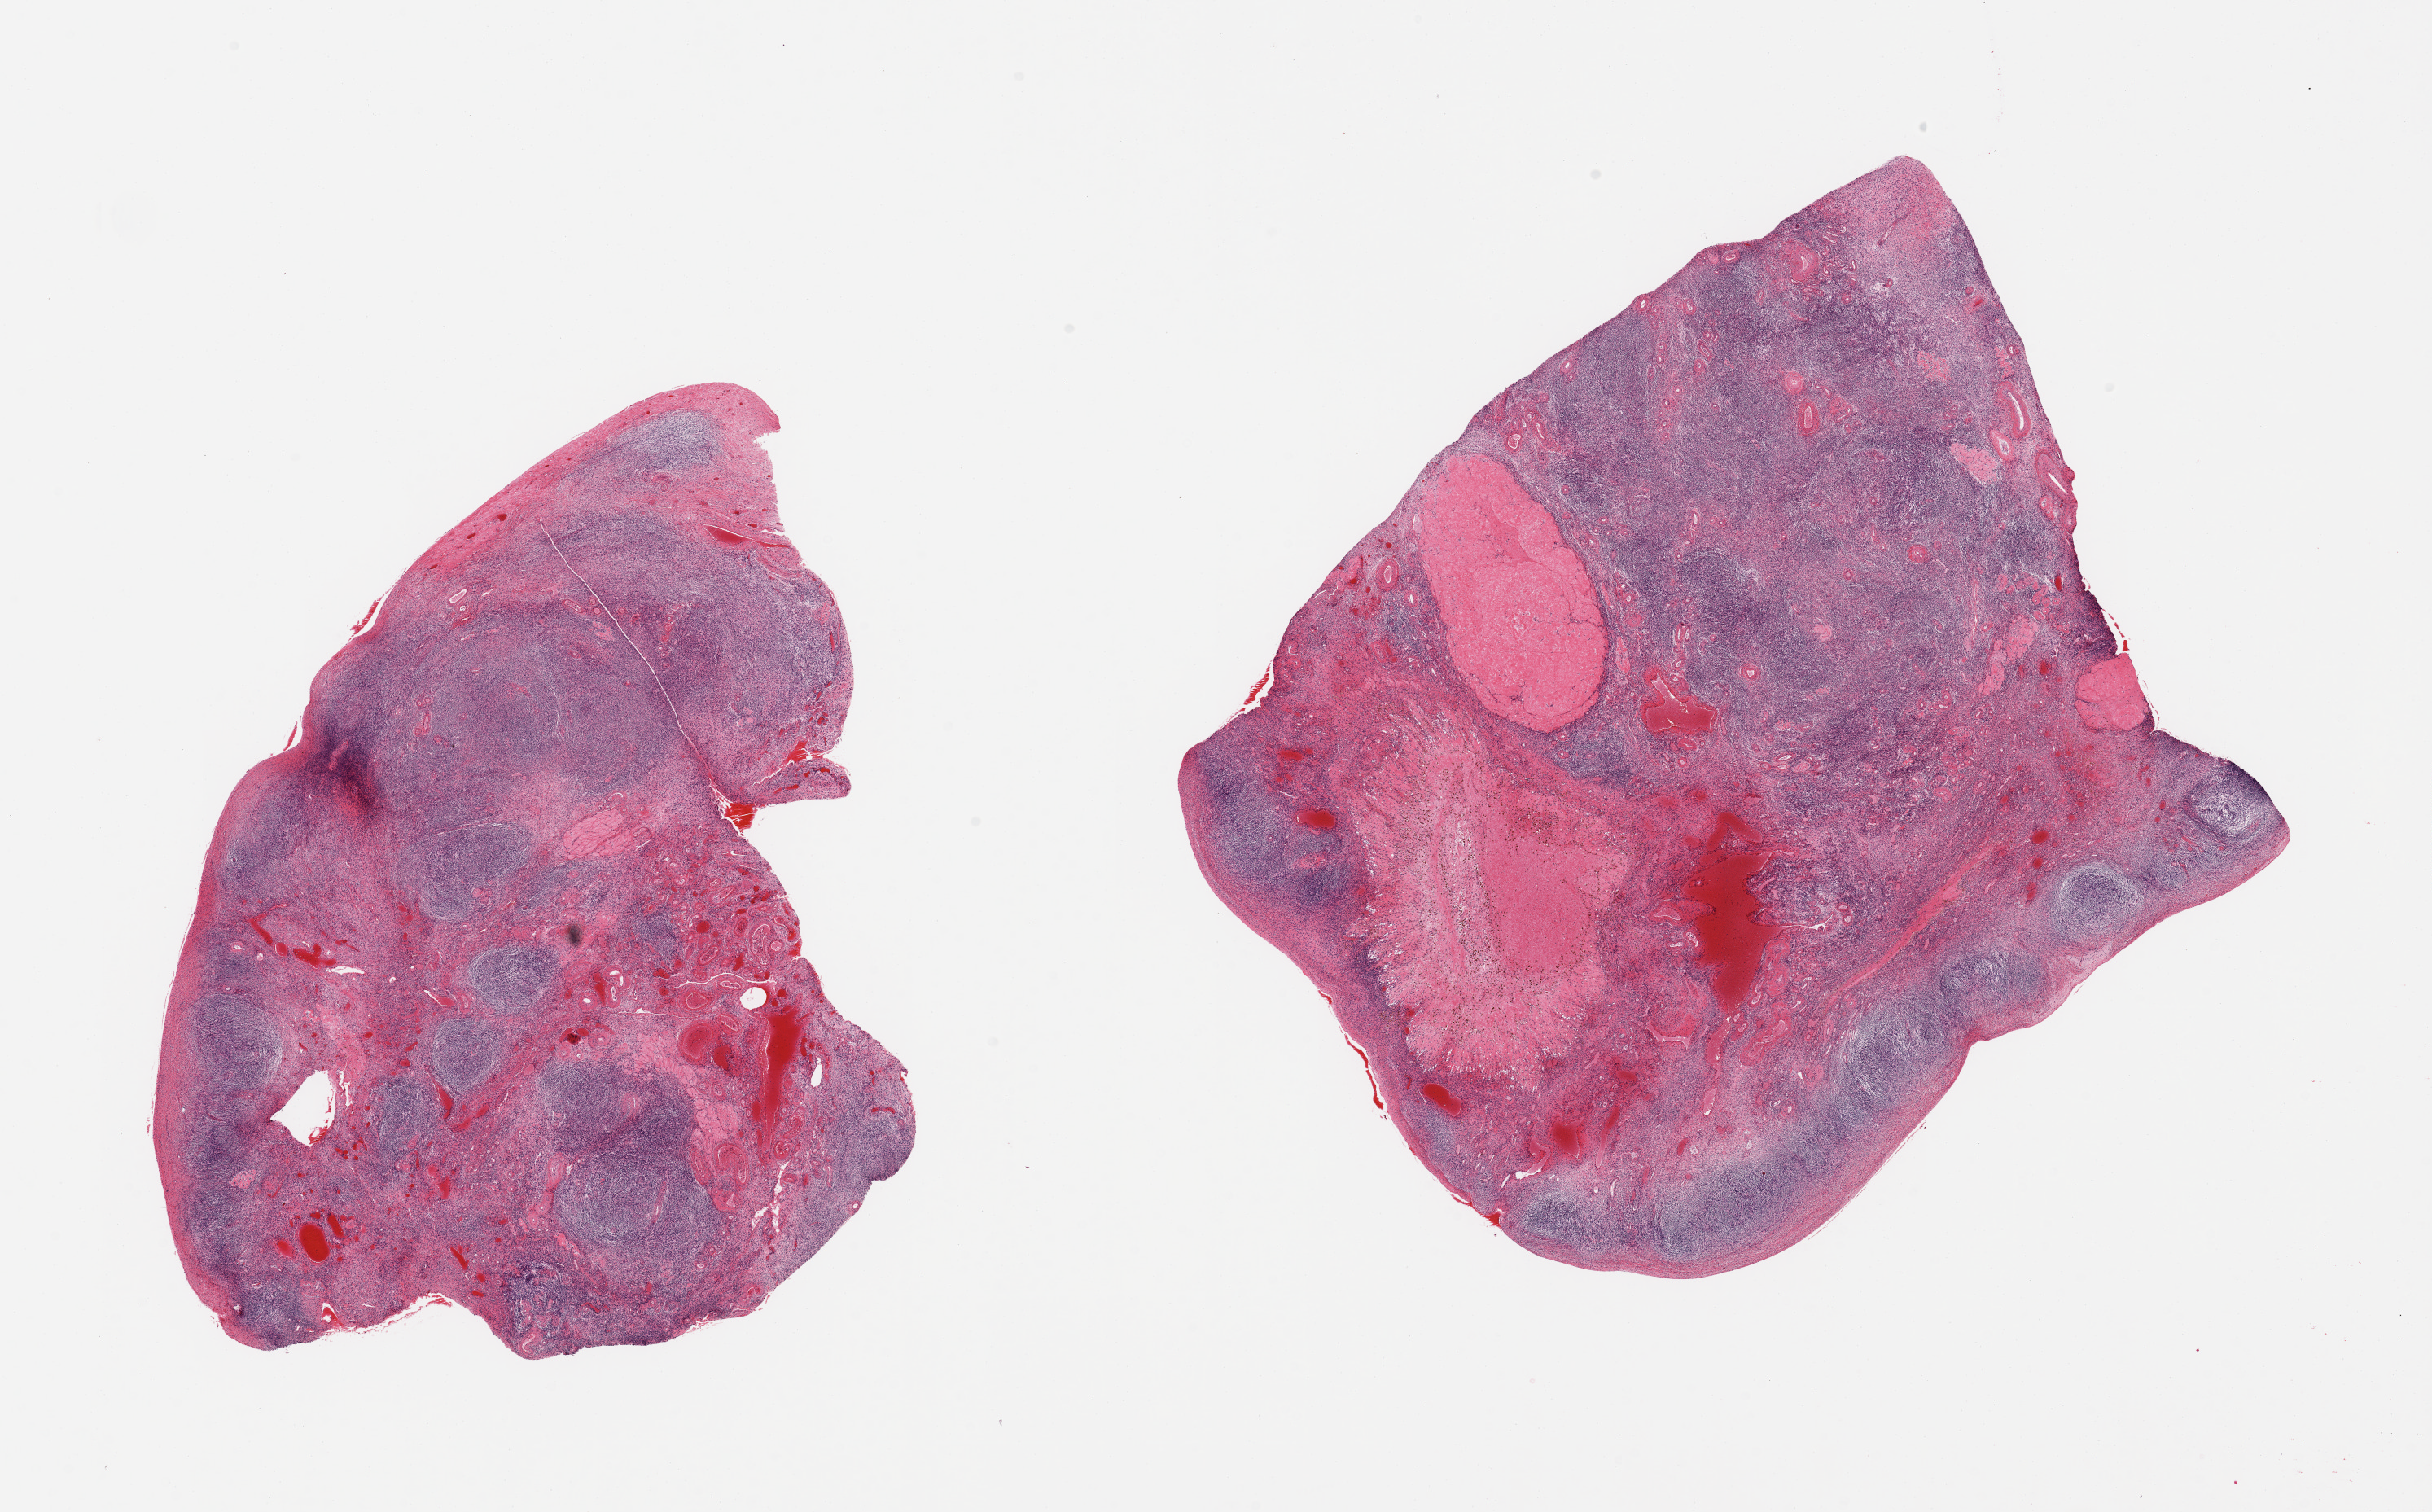
Haematoxylin and eosin whole-slide image — low-resolution overview of the scanned area, about 23.6 x 14.7 mm; PAXgene-fixed, paraffin-embedded tissue; section of ovary (target tissue); donor tissue sample.
Review note (as recorded): 2 pieces; several corpora albicantia.